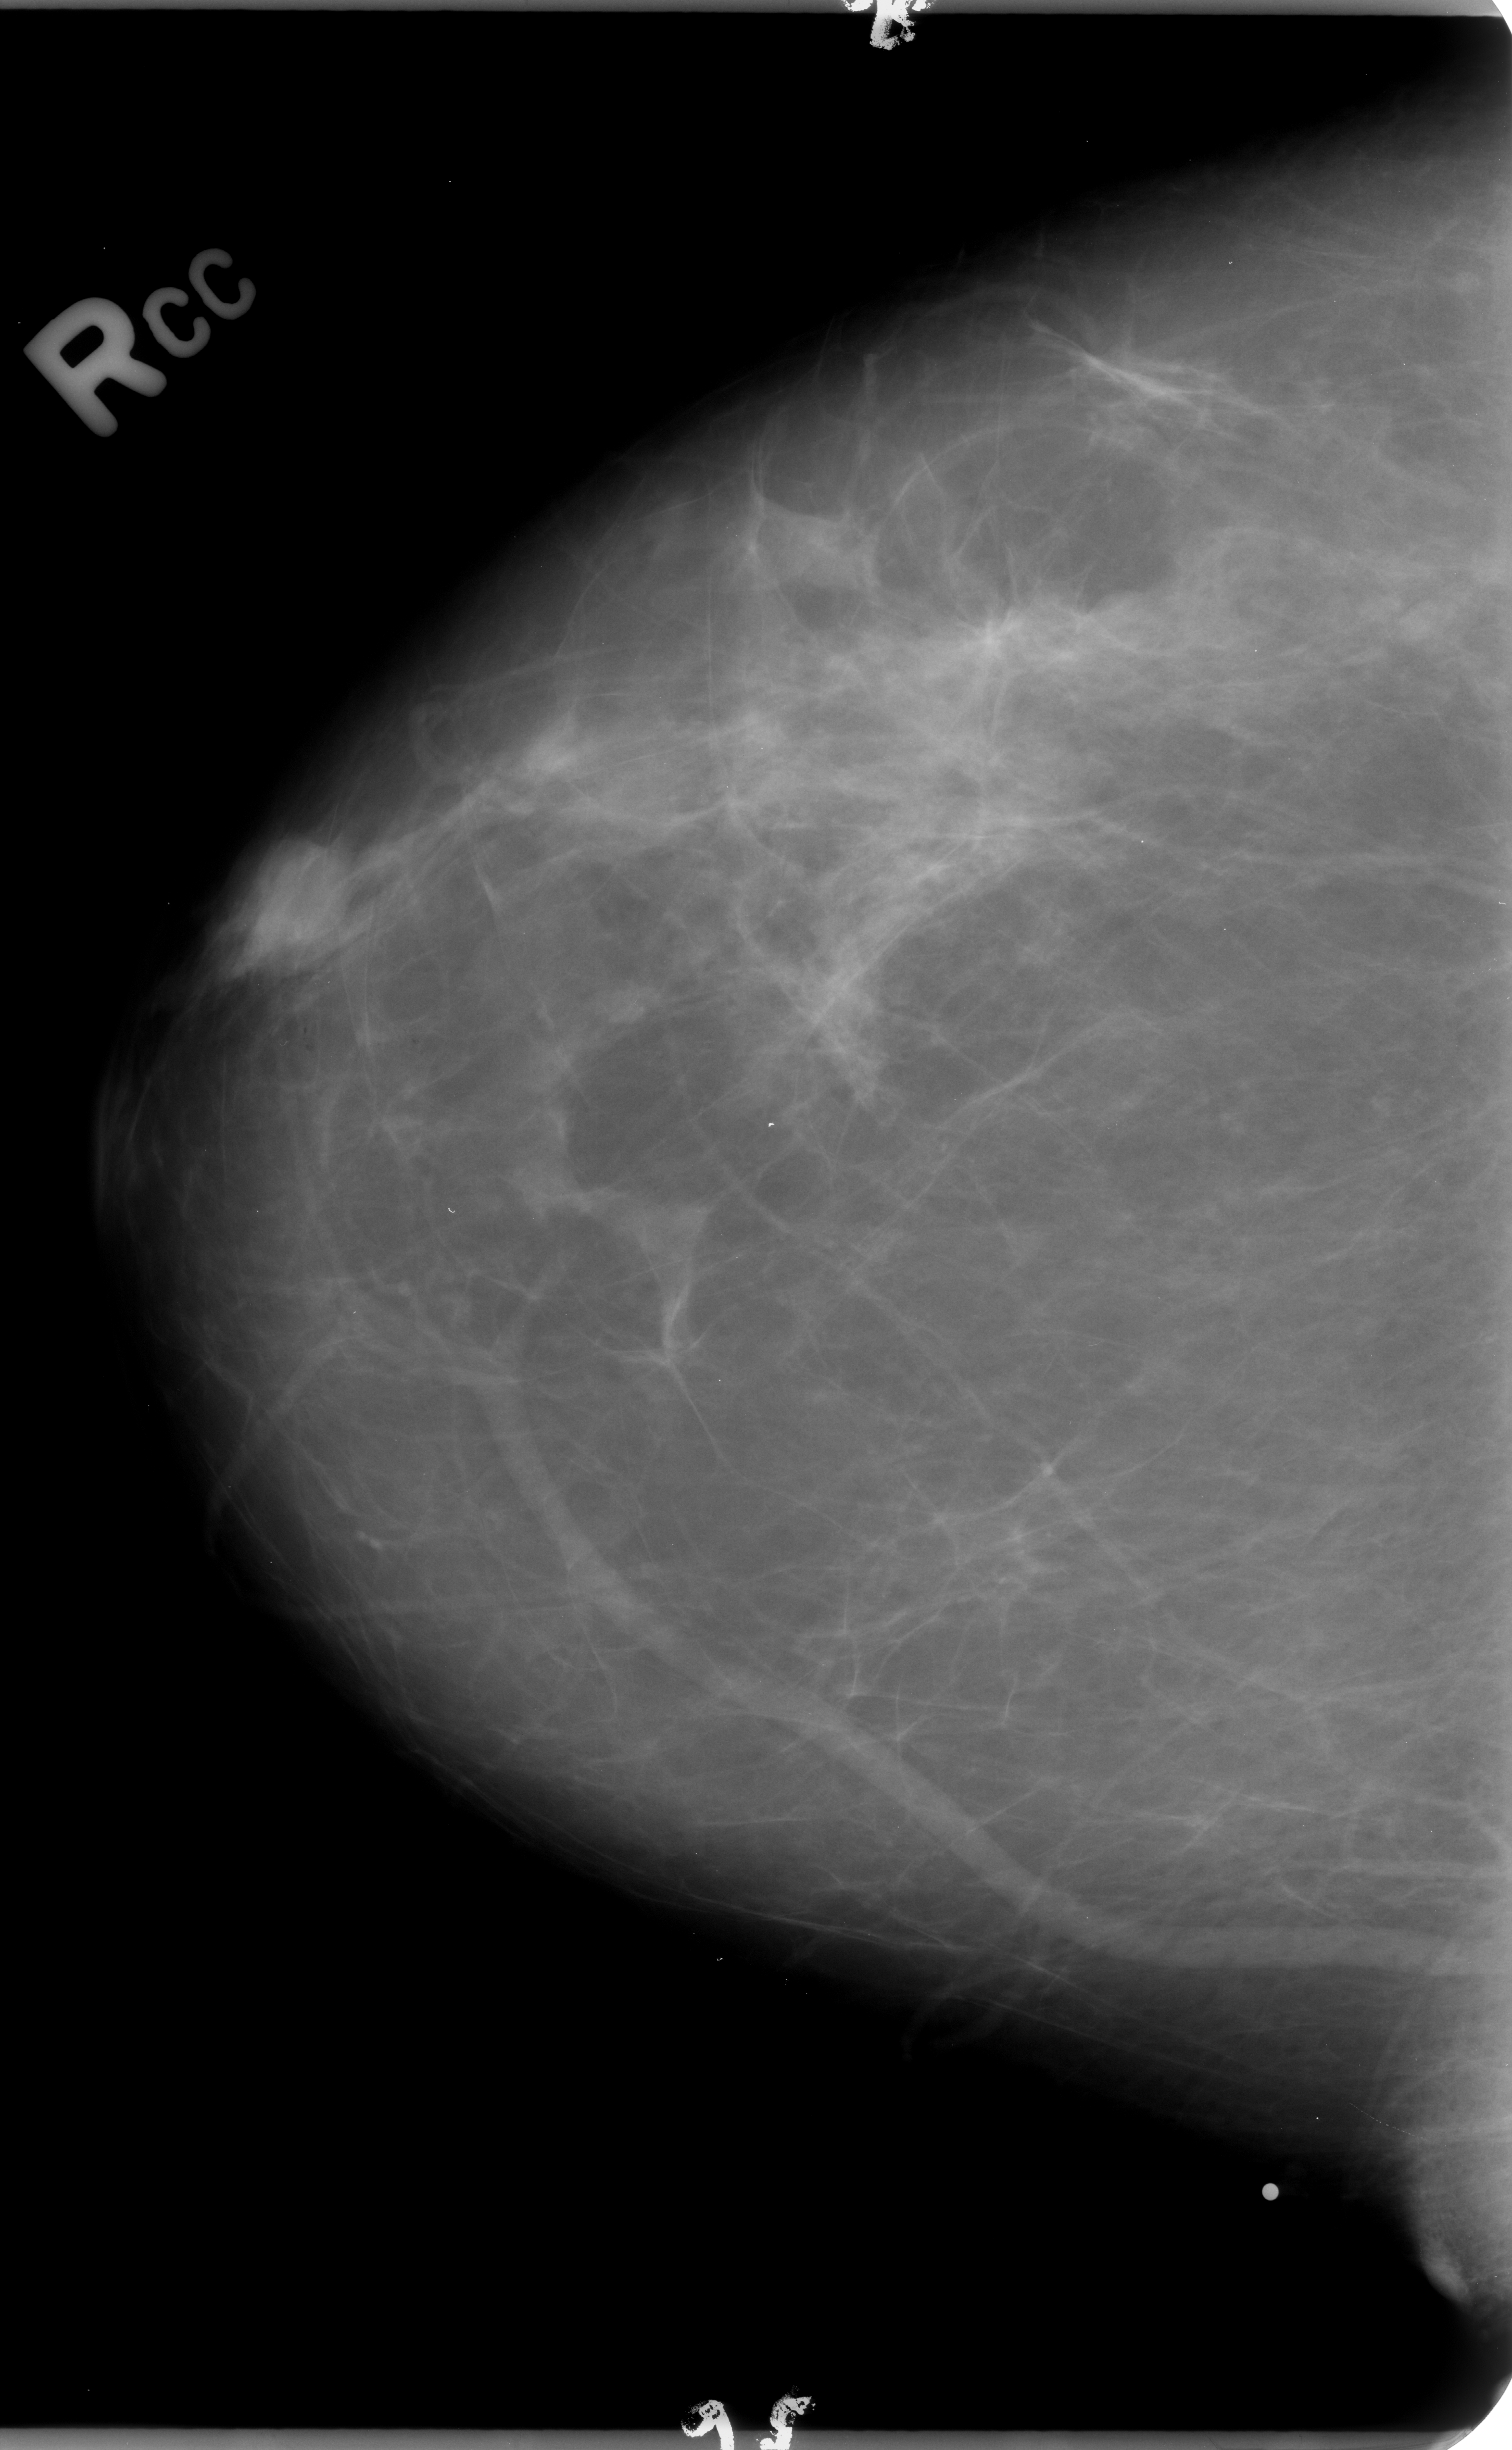
Scanned film-screen mammogram, right breast, CC view, breast composition: scattered fibroglandular densities (BI-RADS density category 2 of 4).
Abnormality record for this image: mass, shape oval, margins circumscribed / ill defined; BI-RADS assessment category 4; subtlety rating 4 on a 1 (subtle) to 5 (obvious) scale; pathology result (as recorded, not read from the image): benign.